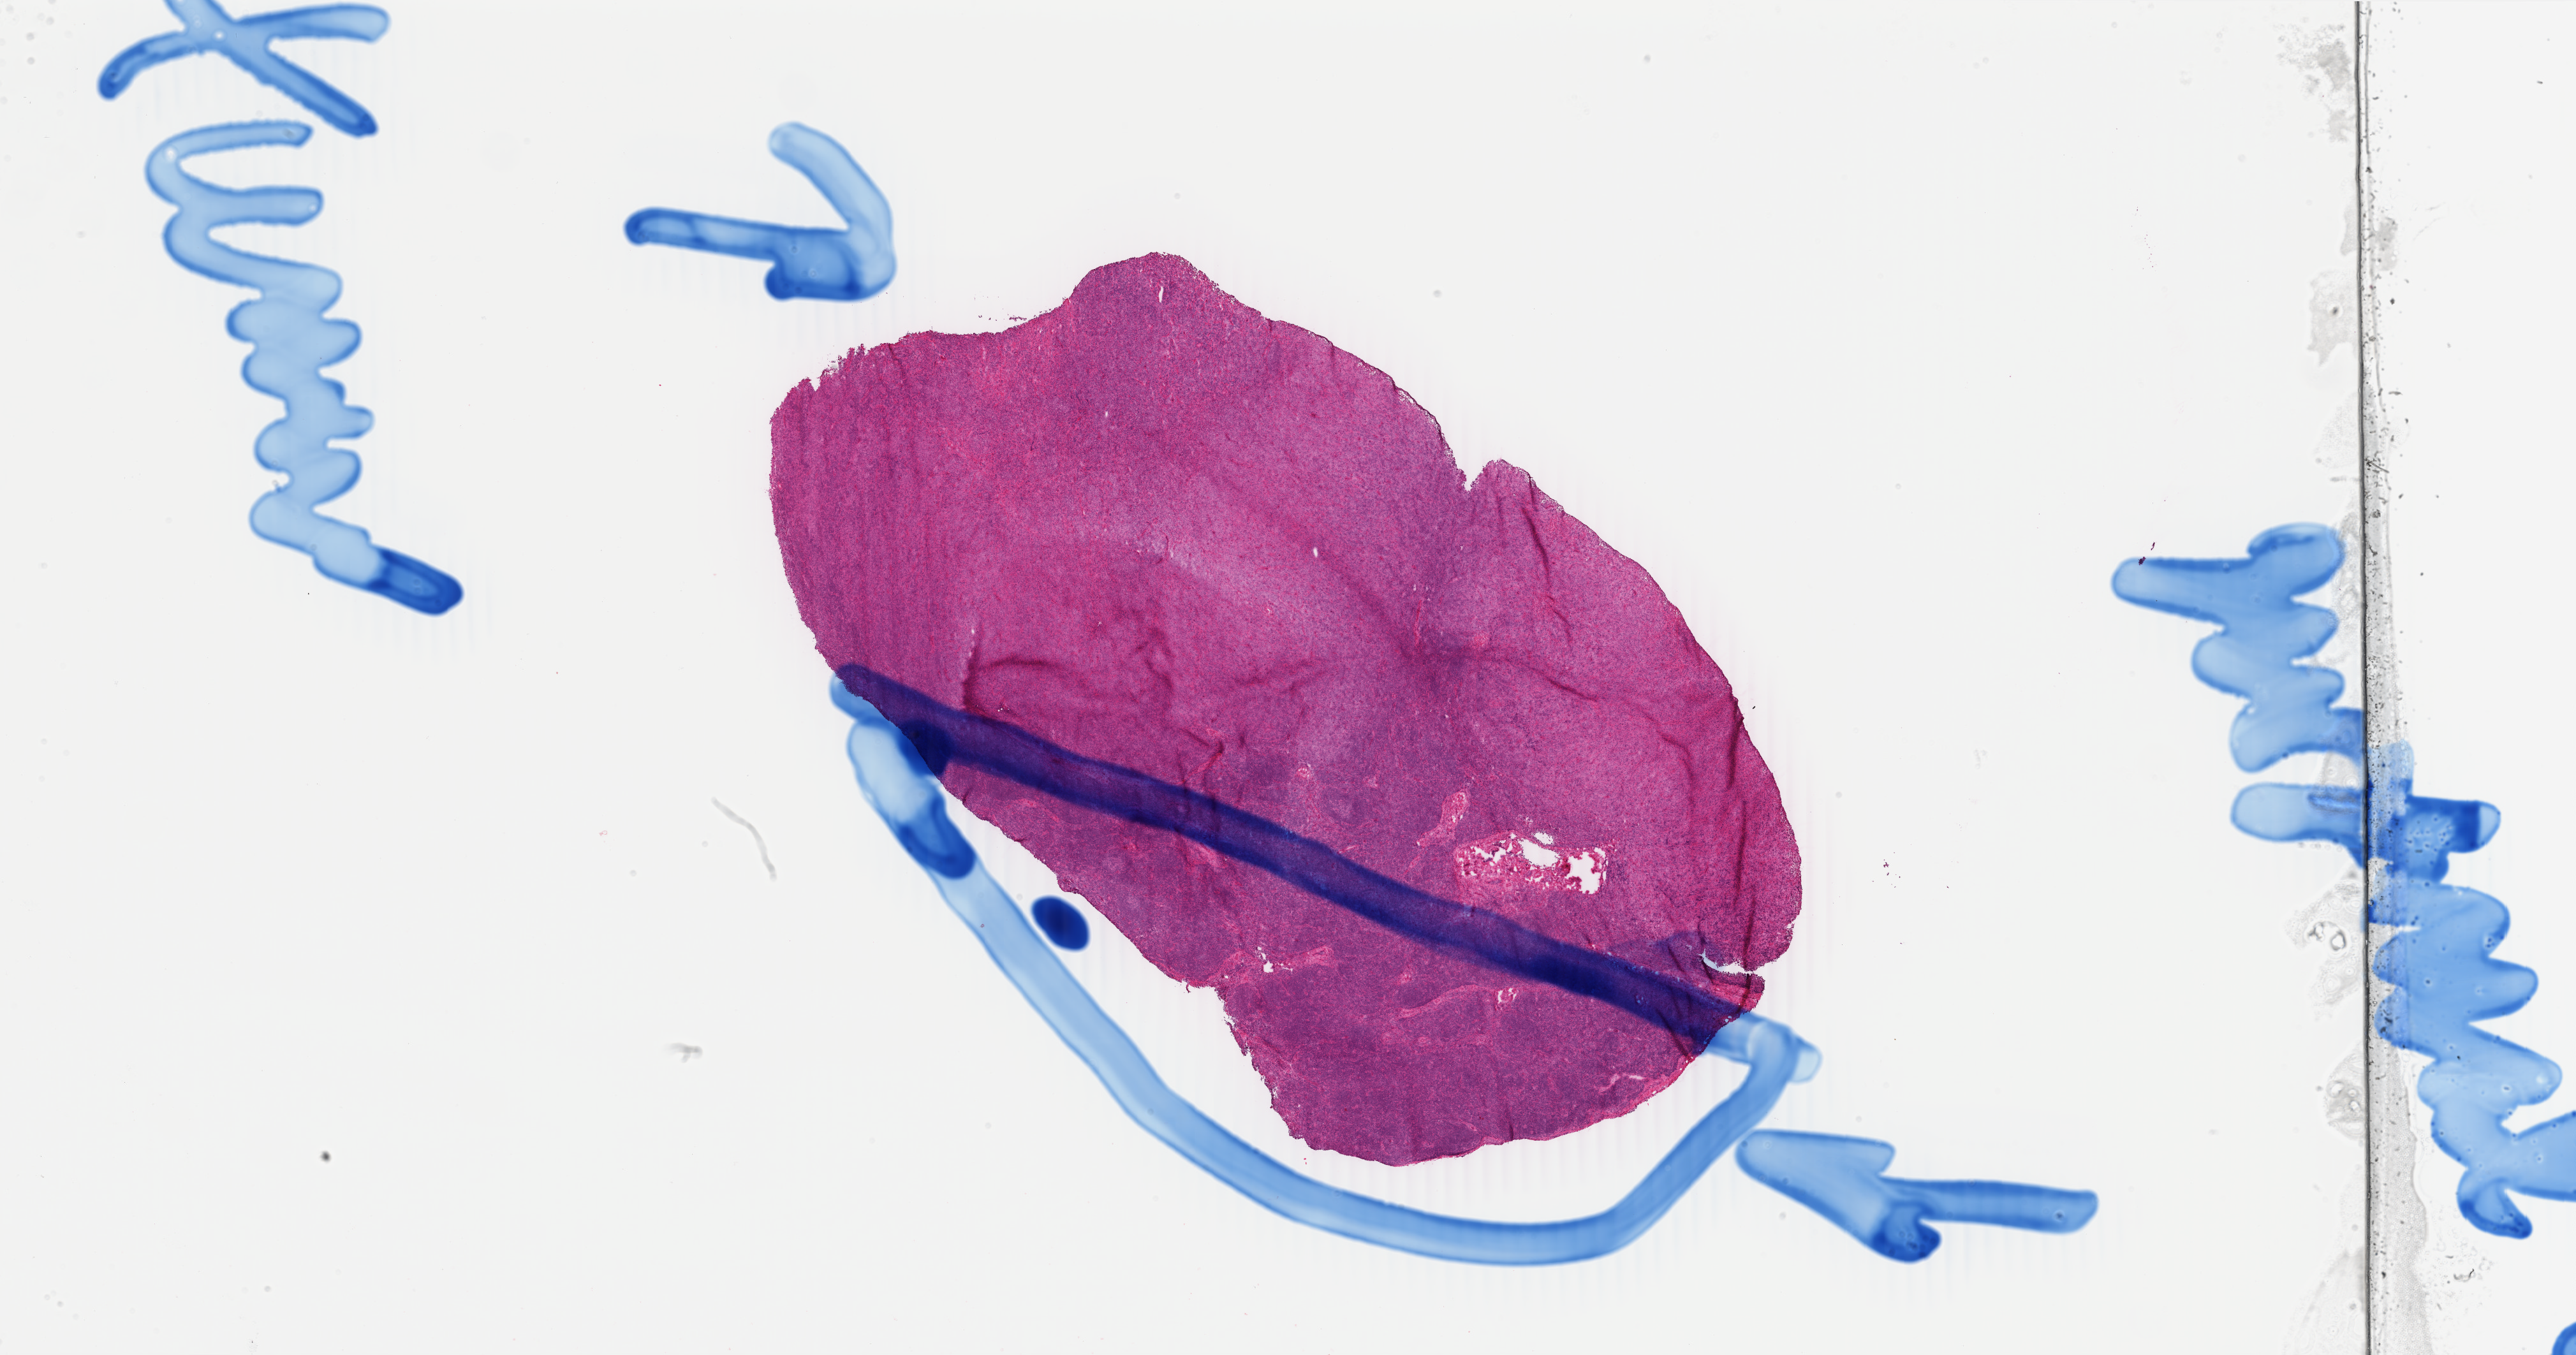
H&E-stained whole-slide image — shown as a low-resolution overview of the whole scanned area (about 32.1 x 16.9 mm, from a 40x scan). Frozen section. Primary tumour sample from the lymphoid tissue. Female patient; age at initial diagnosis 46 years. Composition of this section per pathologist review: tumour cells 80%, tumour nuclei 80%, normal cells 15%, stromal cells 5%, necrosis 0%. Infiltration values recorded for this section: lymphocyte infiltration 20%, monocyte infiltration 5%, neutrophil infiltration 0%.
• histologic diagnosis: Diffuse large B-cell lymphoma, NOS (lymph nodes of head, face and neck)